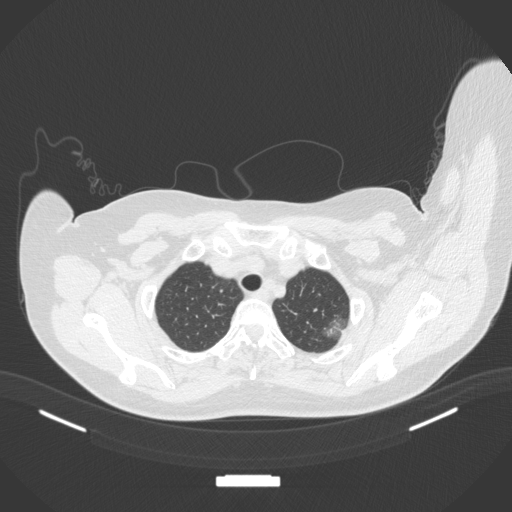
Chest CT, one axial slice. Slice 320 of 386 in the series (ordered by position). Reconstruction kernel B31f. Lung window (W 1500 / L -600 HU). 512 × 512 image matrix, field of view 400 × 400 mm. Patient: female, 58 years. Case-level facts recorded for this patient, not image findings: clinical TNM (as recorded): T1c N0 M0.
Annotated regions visible in this slice (bounding box drawn by a radiologist):
- lung tumour (recorded histology: adenocarcinoma): bounding box (x1, y1, x2, y2) in pixels: (320, 312, 348, 341)